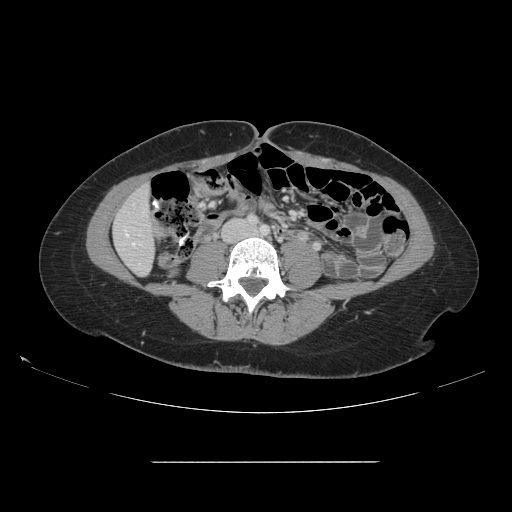
Contrast-enhanced abdominal CT, one axial slice. Position 25 of 151 along the scan axis. Intravenous contrast given. Soft-tissue window (W 400 / L 40 HU). 2.5 mm slice thickness. 512 × 512 image matrix, field of view 421 × 421 mm. Female patient, age 46 years. From the clinical record (not read from this slice): diagnosis: colorectal cancer liver metastases, imaged before liver resection.
Outlined on this slice (expert manual segmentation):
- liver: bounding box <115,188,155,275> (left, top, right, bottom; pixels)
- planned liver remnant (the part of the liver to remain after resection): <115,188,155,275>